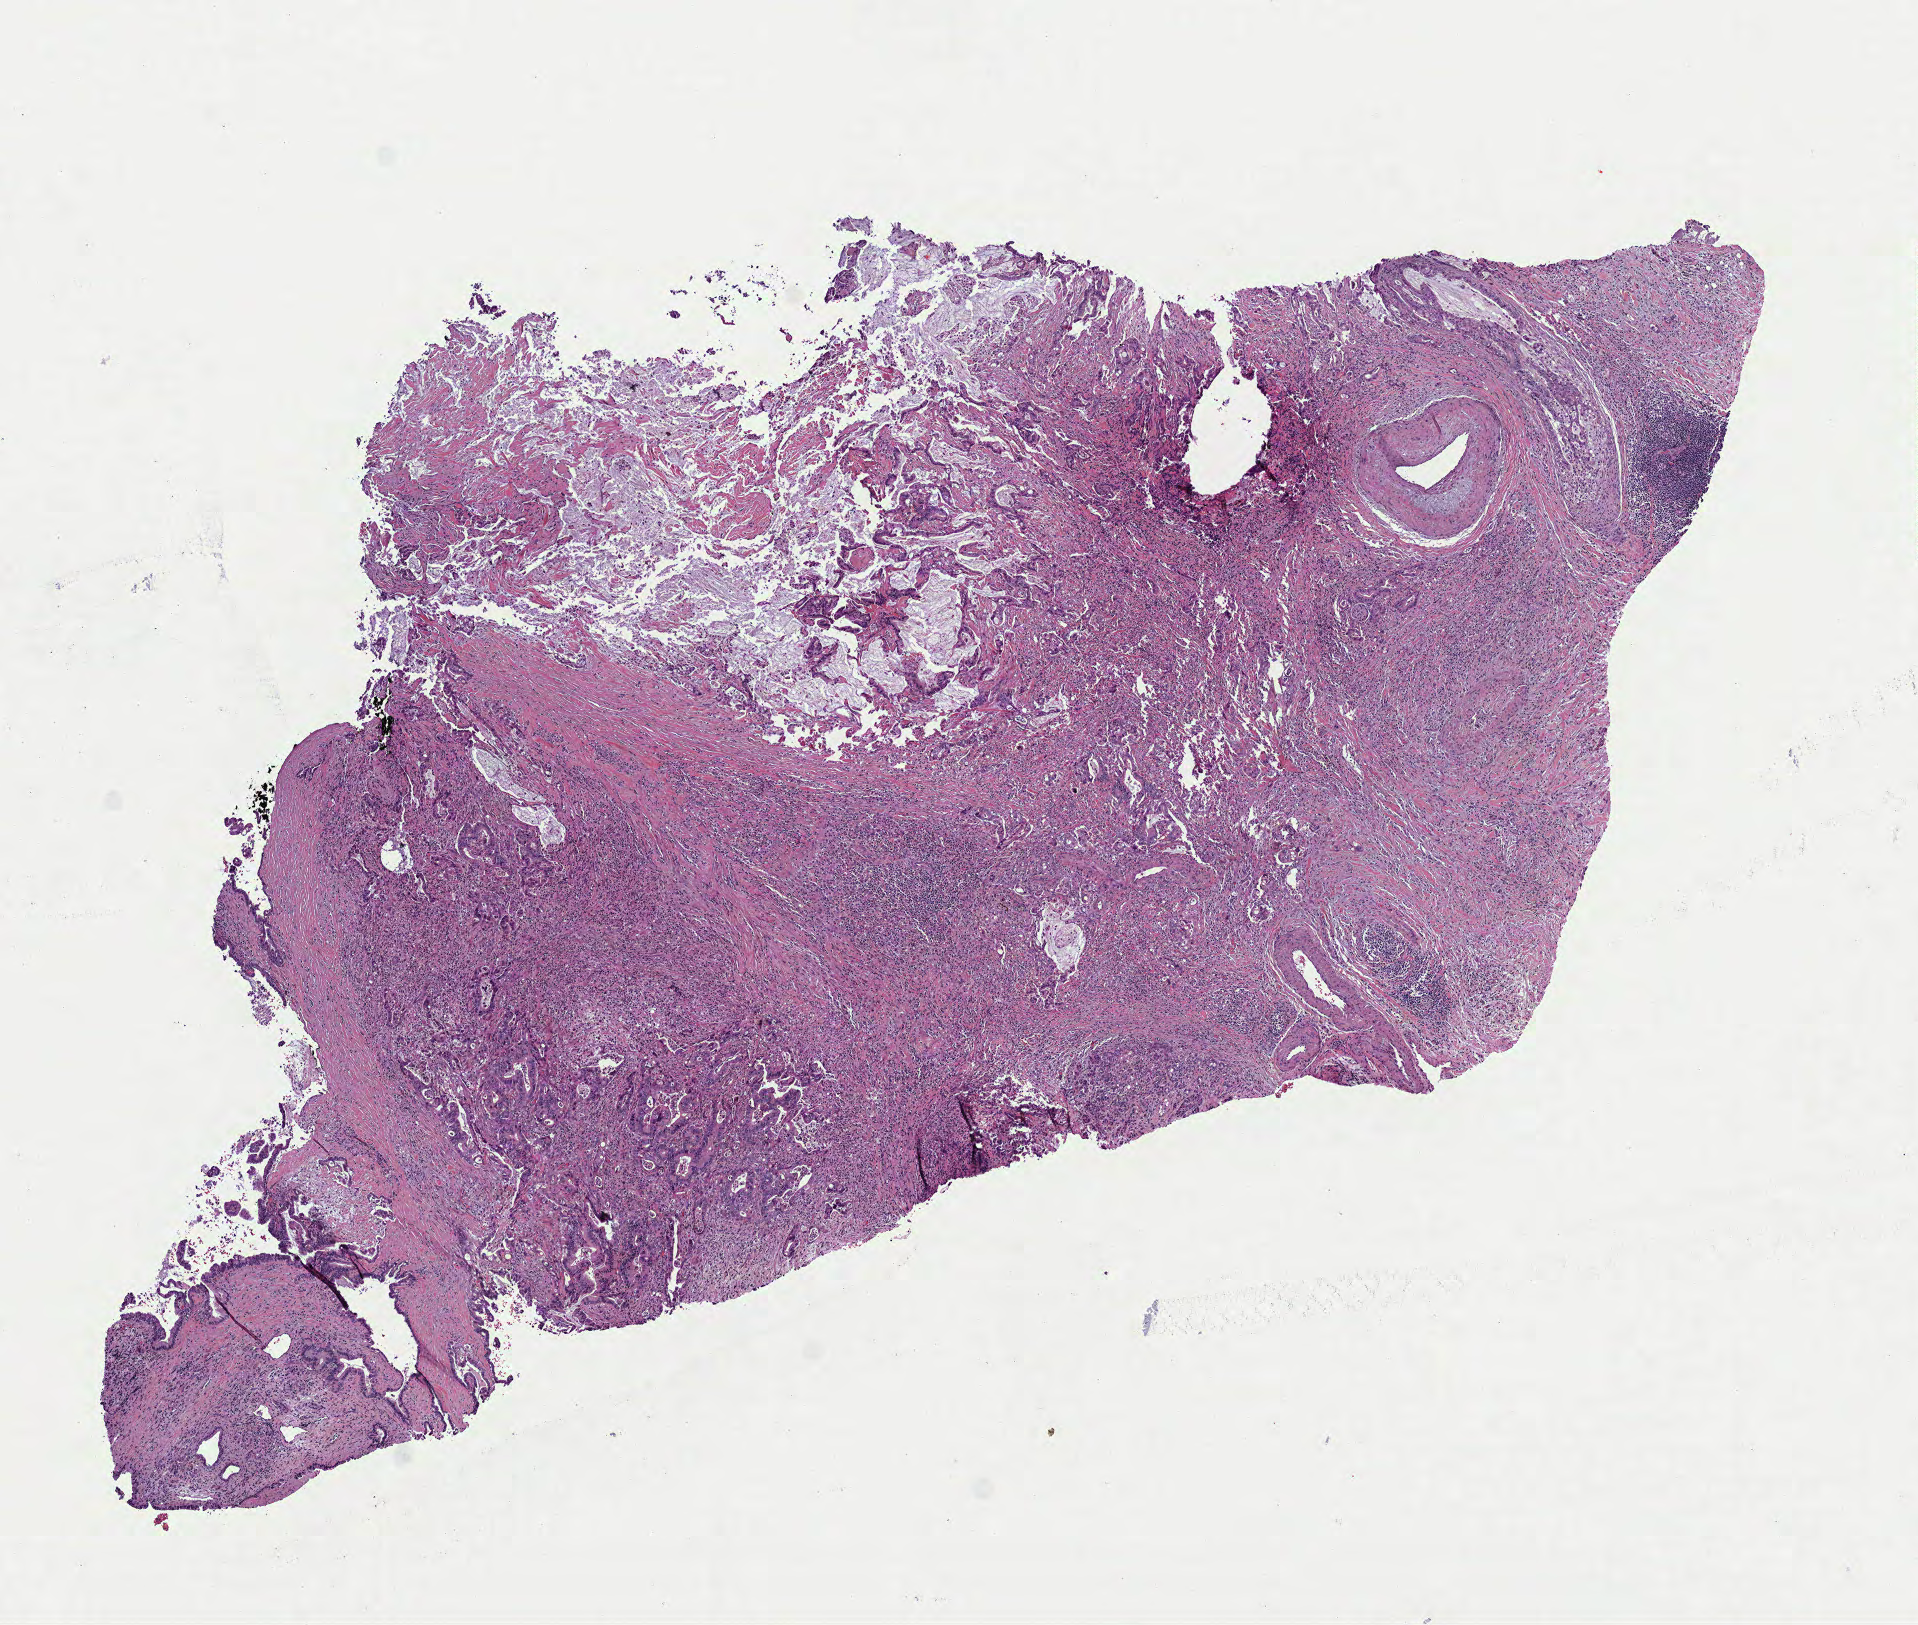
Digitized H&E tissue section (whole slide), a low-resolution overview of the entire scanned area, about 7.7 x 6.6 mm. Formalin-fixed paraffin-embedded (FFPE) diagnostic section. Primary tumour sample from the pancreas. Female patient; age at initial diagnosis 55 years. Histologic grade: G2 (moderately differentiated).
Lymph nodes positive (case pathology): 1 of 19 examined. Diagnosis: Adenocarcinoma, NOS (head of pancreas). AJCC pathologic stage: IIB.